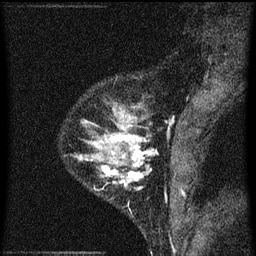
Breast MRI (dynamic contrast-enhanced), one sagittal slice; position 19 of 60 along the scan axis; dynamic contrast-enhanced series, image 2 of 3 at this slice position (ordered by acquisition); 1.5 T; TE 4.2 ms, TR 8 ms; 256 × 256 image matrix, field of view 180 × 180 mm. Female patient, age 33 years.
Structures marked on this image (semi-automatic segmentation, software-assisted and operator-edited):
- analysis volume of interest (the breast-tissue region the enhancement analysis was run in; not a lesion): bounding box (x1, y1, x2, y2) in pixels: (75, 118, 152, 191)
- tumour enhancement mask (voxels above the 70 % enhancement threshold inside the analysis volume of interest): (79, 126, 147, 187)